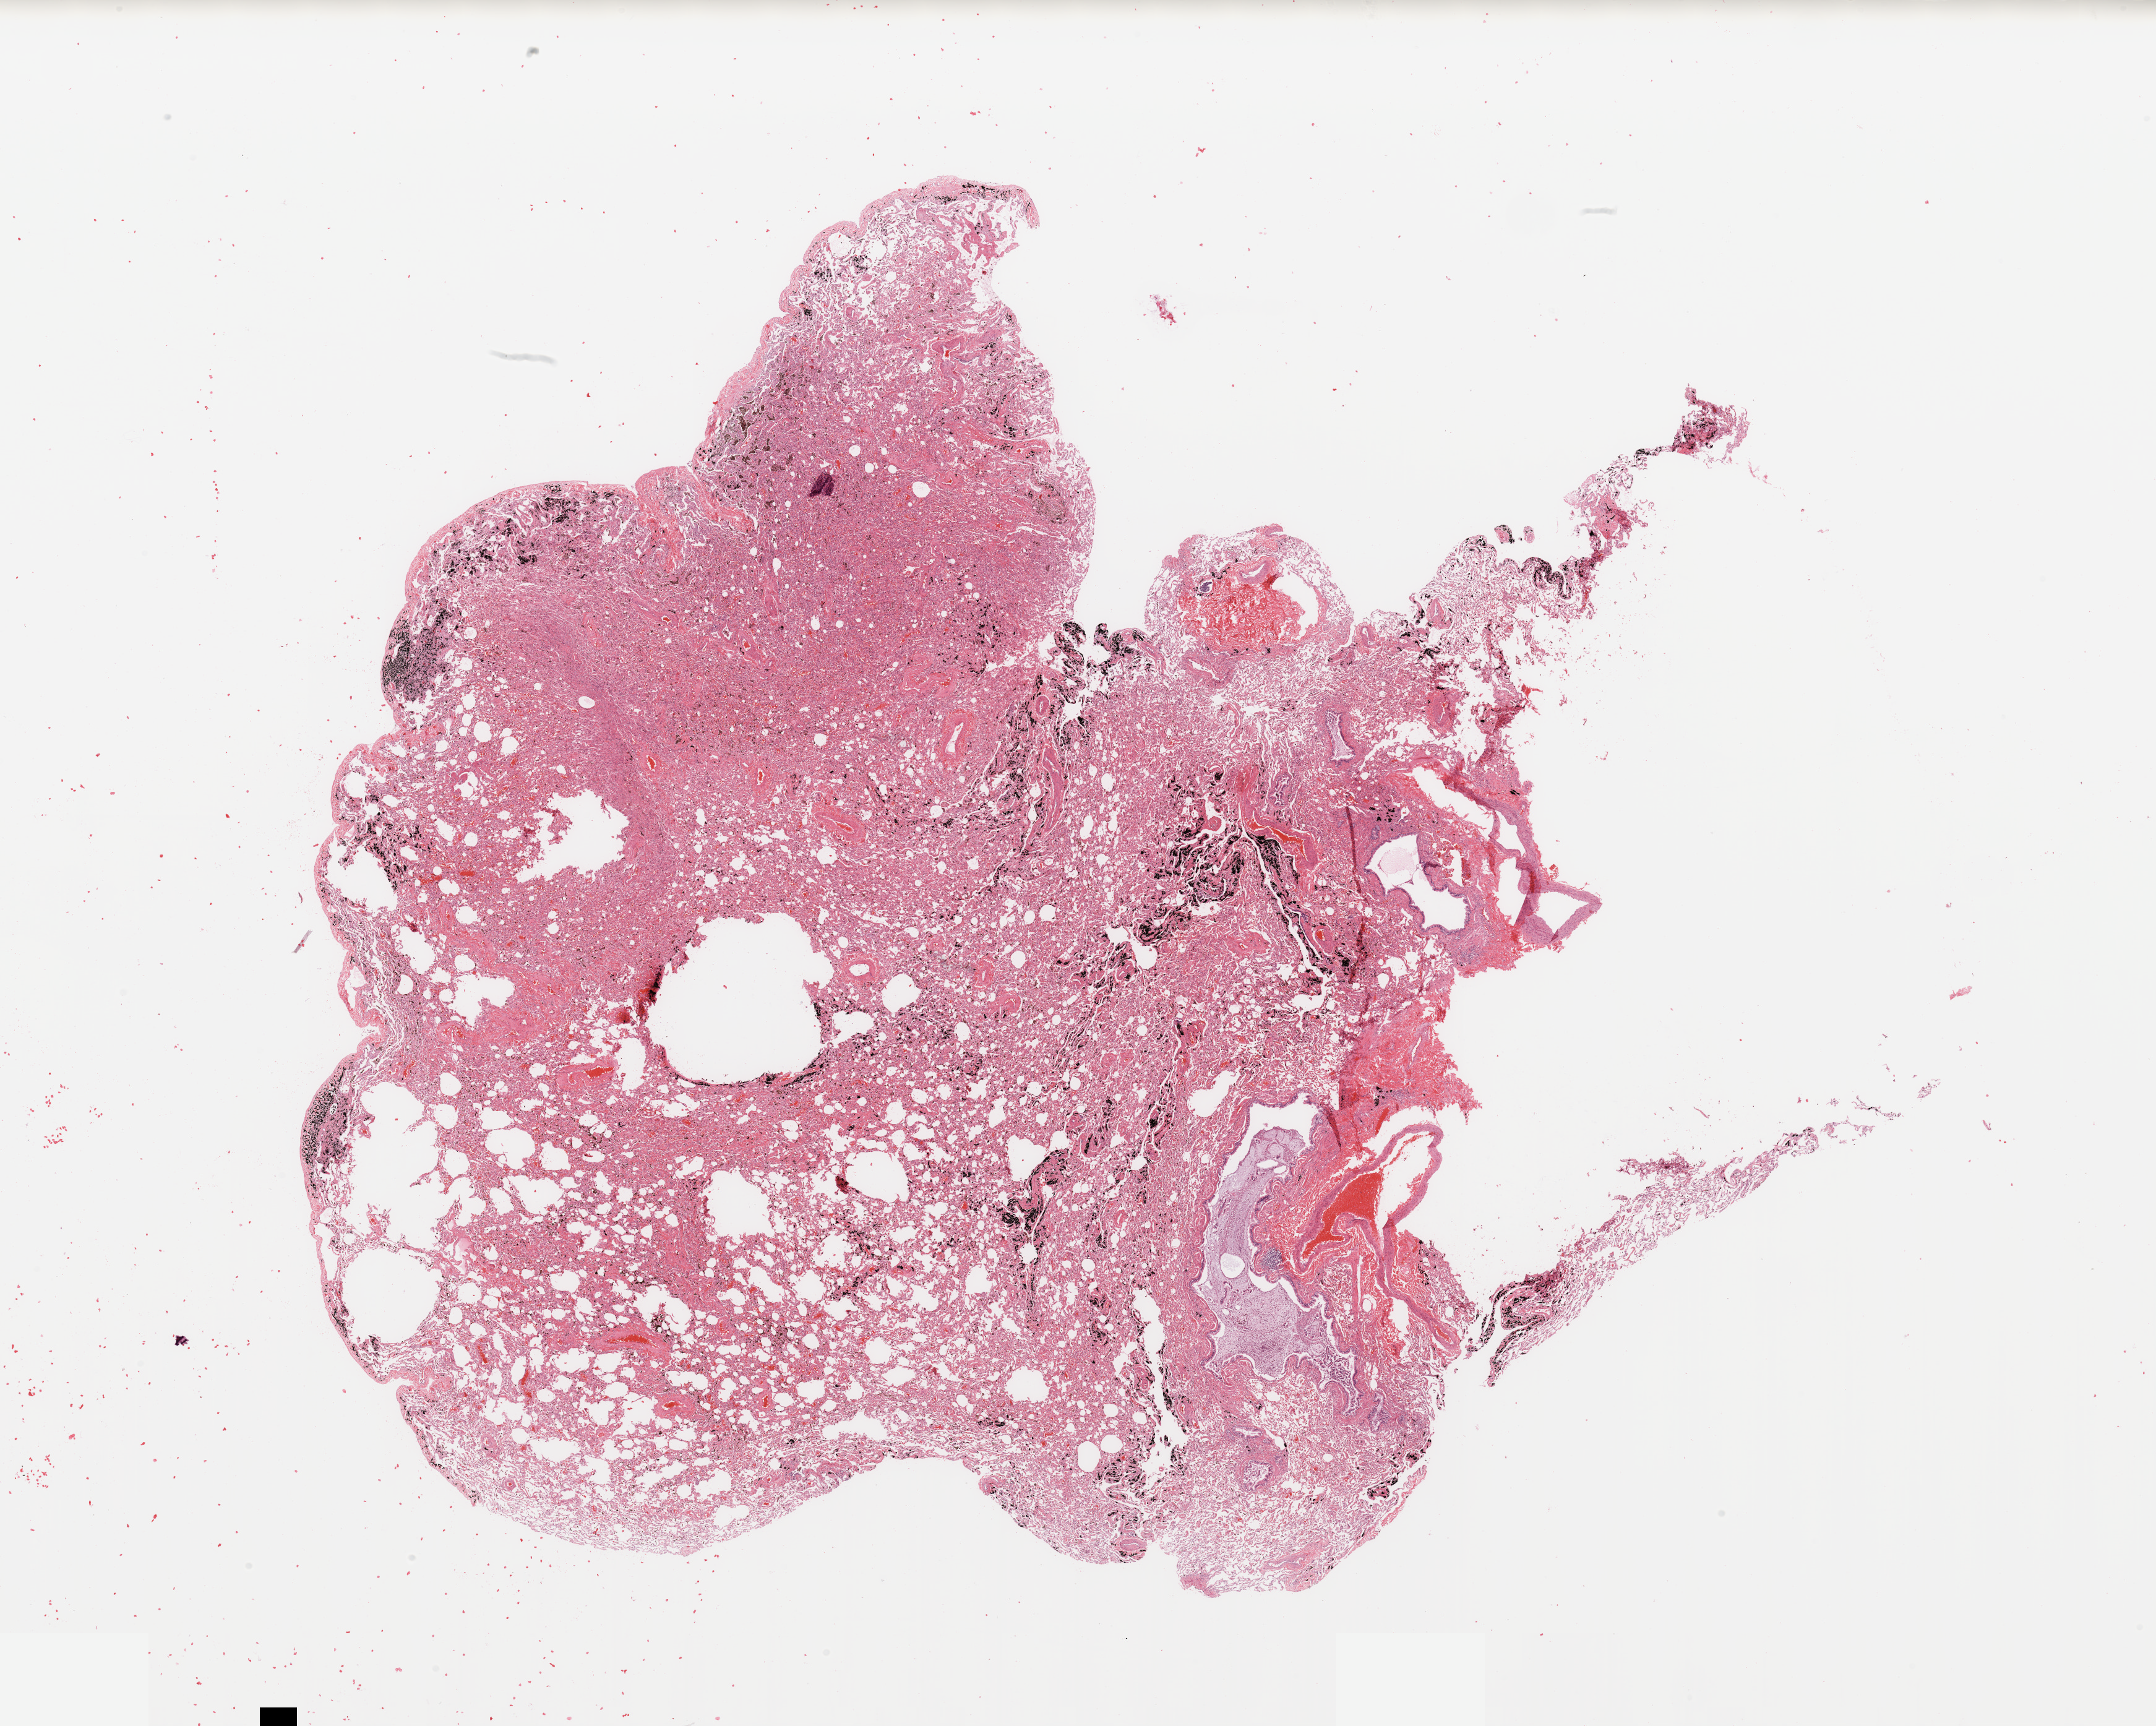
H&E whole-slide image — shown as a low-resolution overview of the whole scanned area (about 27.6 x 22.1 mm, from a 20x scan); normal (non-tumour) tissue sample, sampled site: lung. Patient: male, age 54 years.
This section: normal (non-tumour) tissue from the same patient. Patient diagnosis: Adenocarcinoma, NOS.